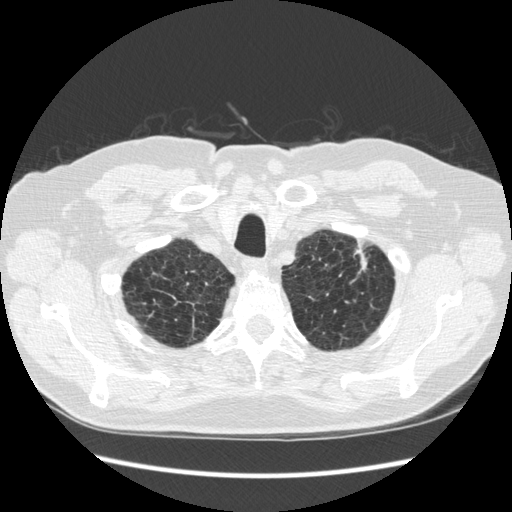
Chest CT (low-dose screening protocol), one axial image, third screening round (two years after baseline), lung window (W 1500 / L -600 HU), 1.25 mm slice thickness, 120 kVp, 512 × 512 image matrix. Male, age 70 years at enrolment. Former smoker at enrolment.
Lesion marked by an expert reader, bounding box [x1, y1, x2, y2] px = [324, 235, 380, 300]. The screening reader recorded 2 non-calcified nodules or masses ≥4 mm on this exam (left upper lobe, right lower lobe); which of them this box marks is not recorded. Lung cancer was diagnosed 92 days after this screen: squamous cell carcinoma, NOS, left upper lobe, moderately differentiated (G2), stage IA (AJCC 6th edition), 18 mm at pathology.